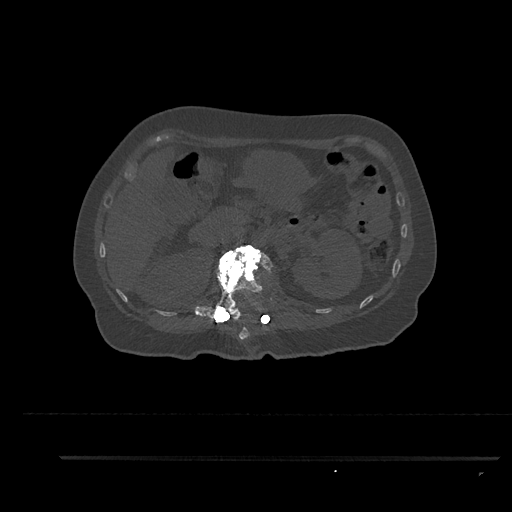
CT including the spine, one axial slice. Slice 227 of 797 in the series (ordered by position). Reconstruction kernel Br40s/3. Bone window (W 1800 / L 400 HU). 0.5 mm slice thickness. 512 × 512 image matrix, field of view 408 × 408 mm. Patient: female, 44 years. From the clinical record (not read from this slice): primary cancer: renal.
Annotated regions visible in this slice (semi-automatic segmentation, software-assisted and operator-edited):
- L1 vertebra: bounding box <207,243,273,323> (left, top, right, bottom; pixels)
- T12 vertebra: <229,310,251,340>